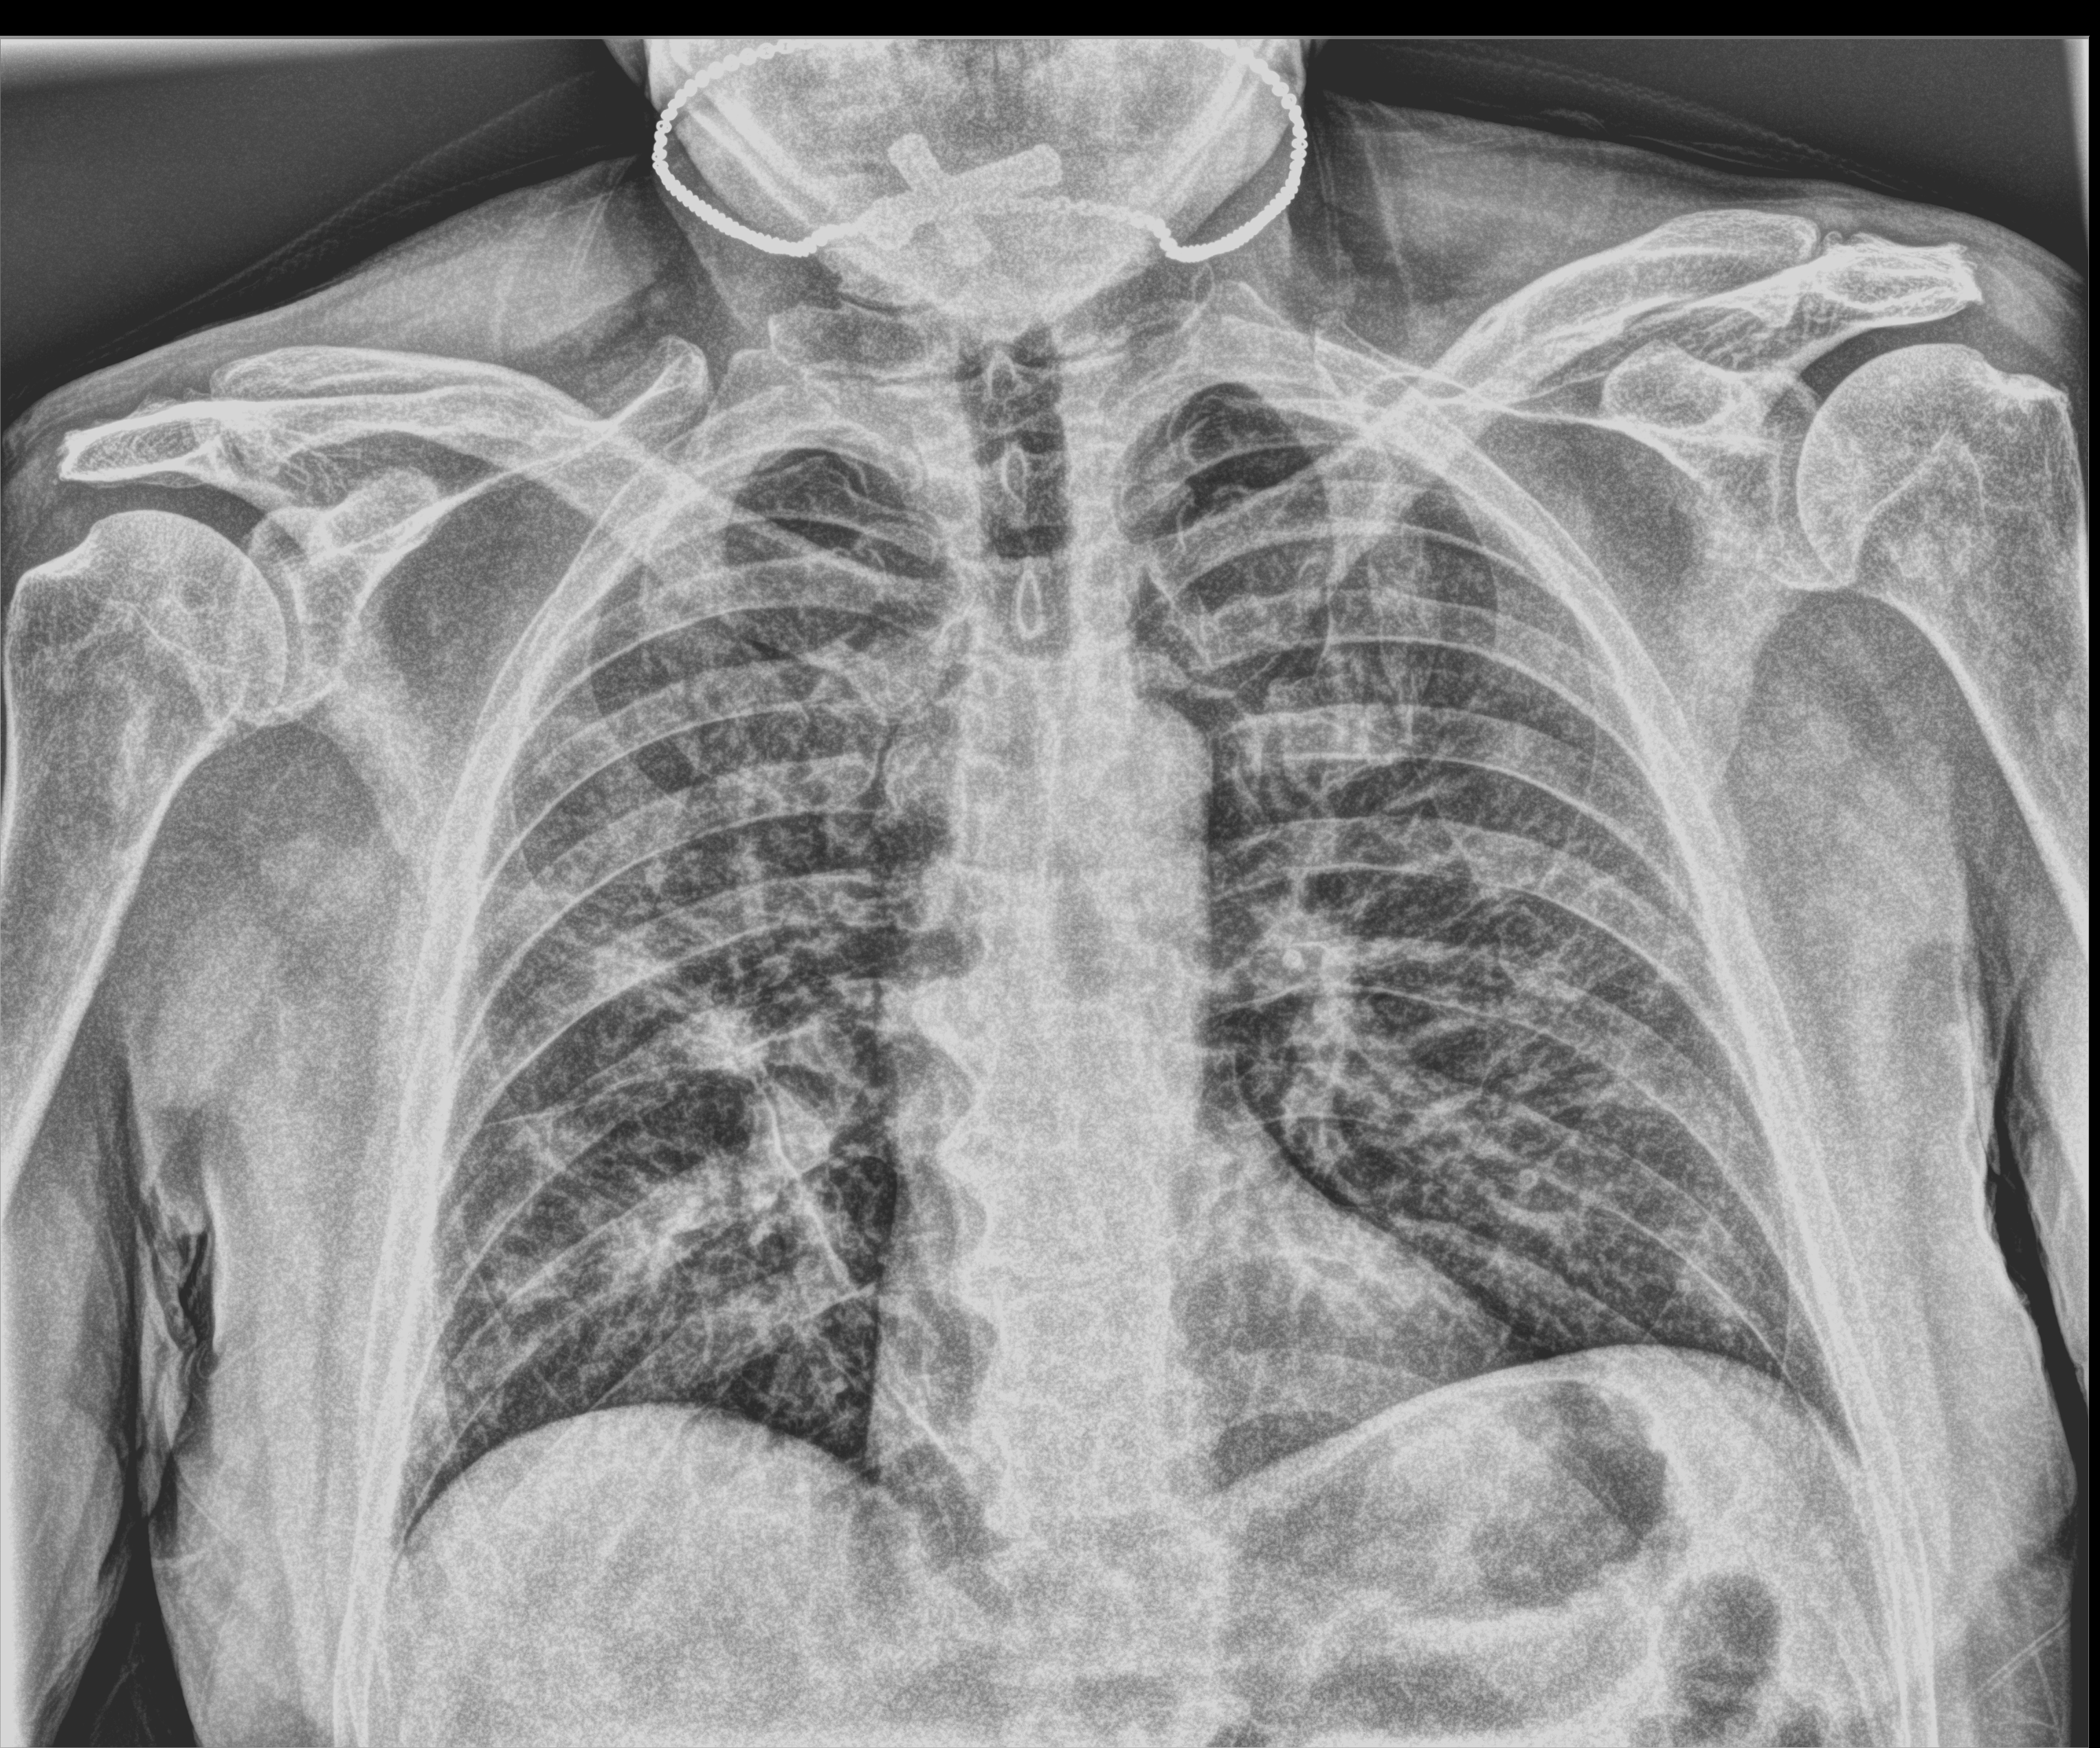
Portable chest radiograph, anteroposterior (AP) projection. Male patient hospitalised with COVID-19, age 18–59 years.
Admission-level facts for this patient (not findings on this image; timing relative to this image not recorded):
- mechanically ventilated during this hospital stay: no
- length of hospital stay: 5 days
- COPD (admission record): no